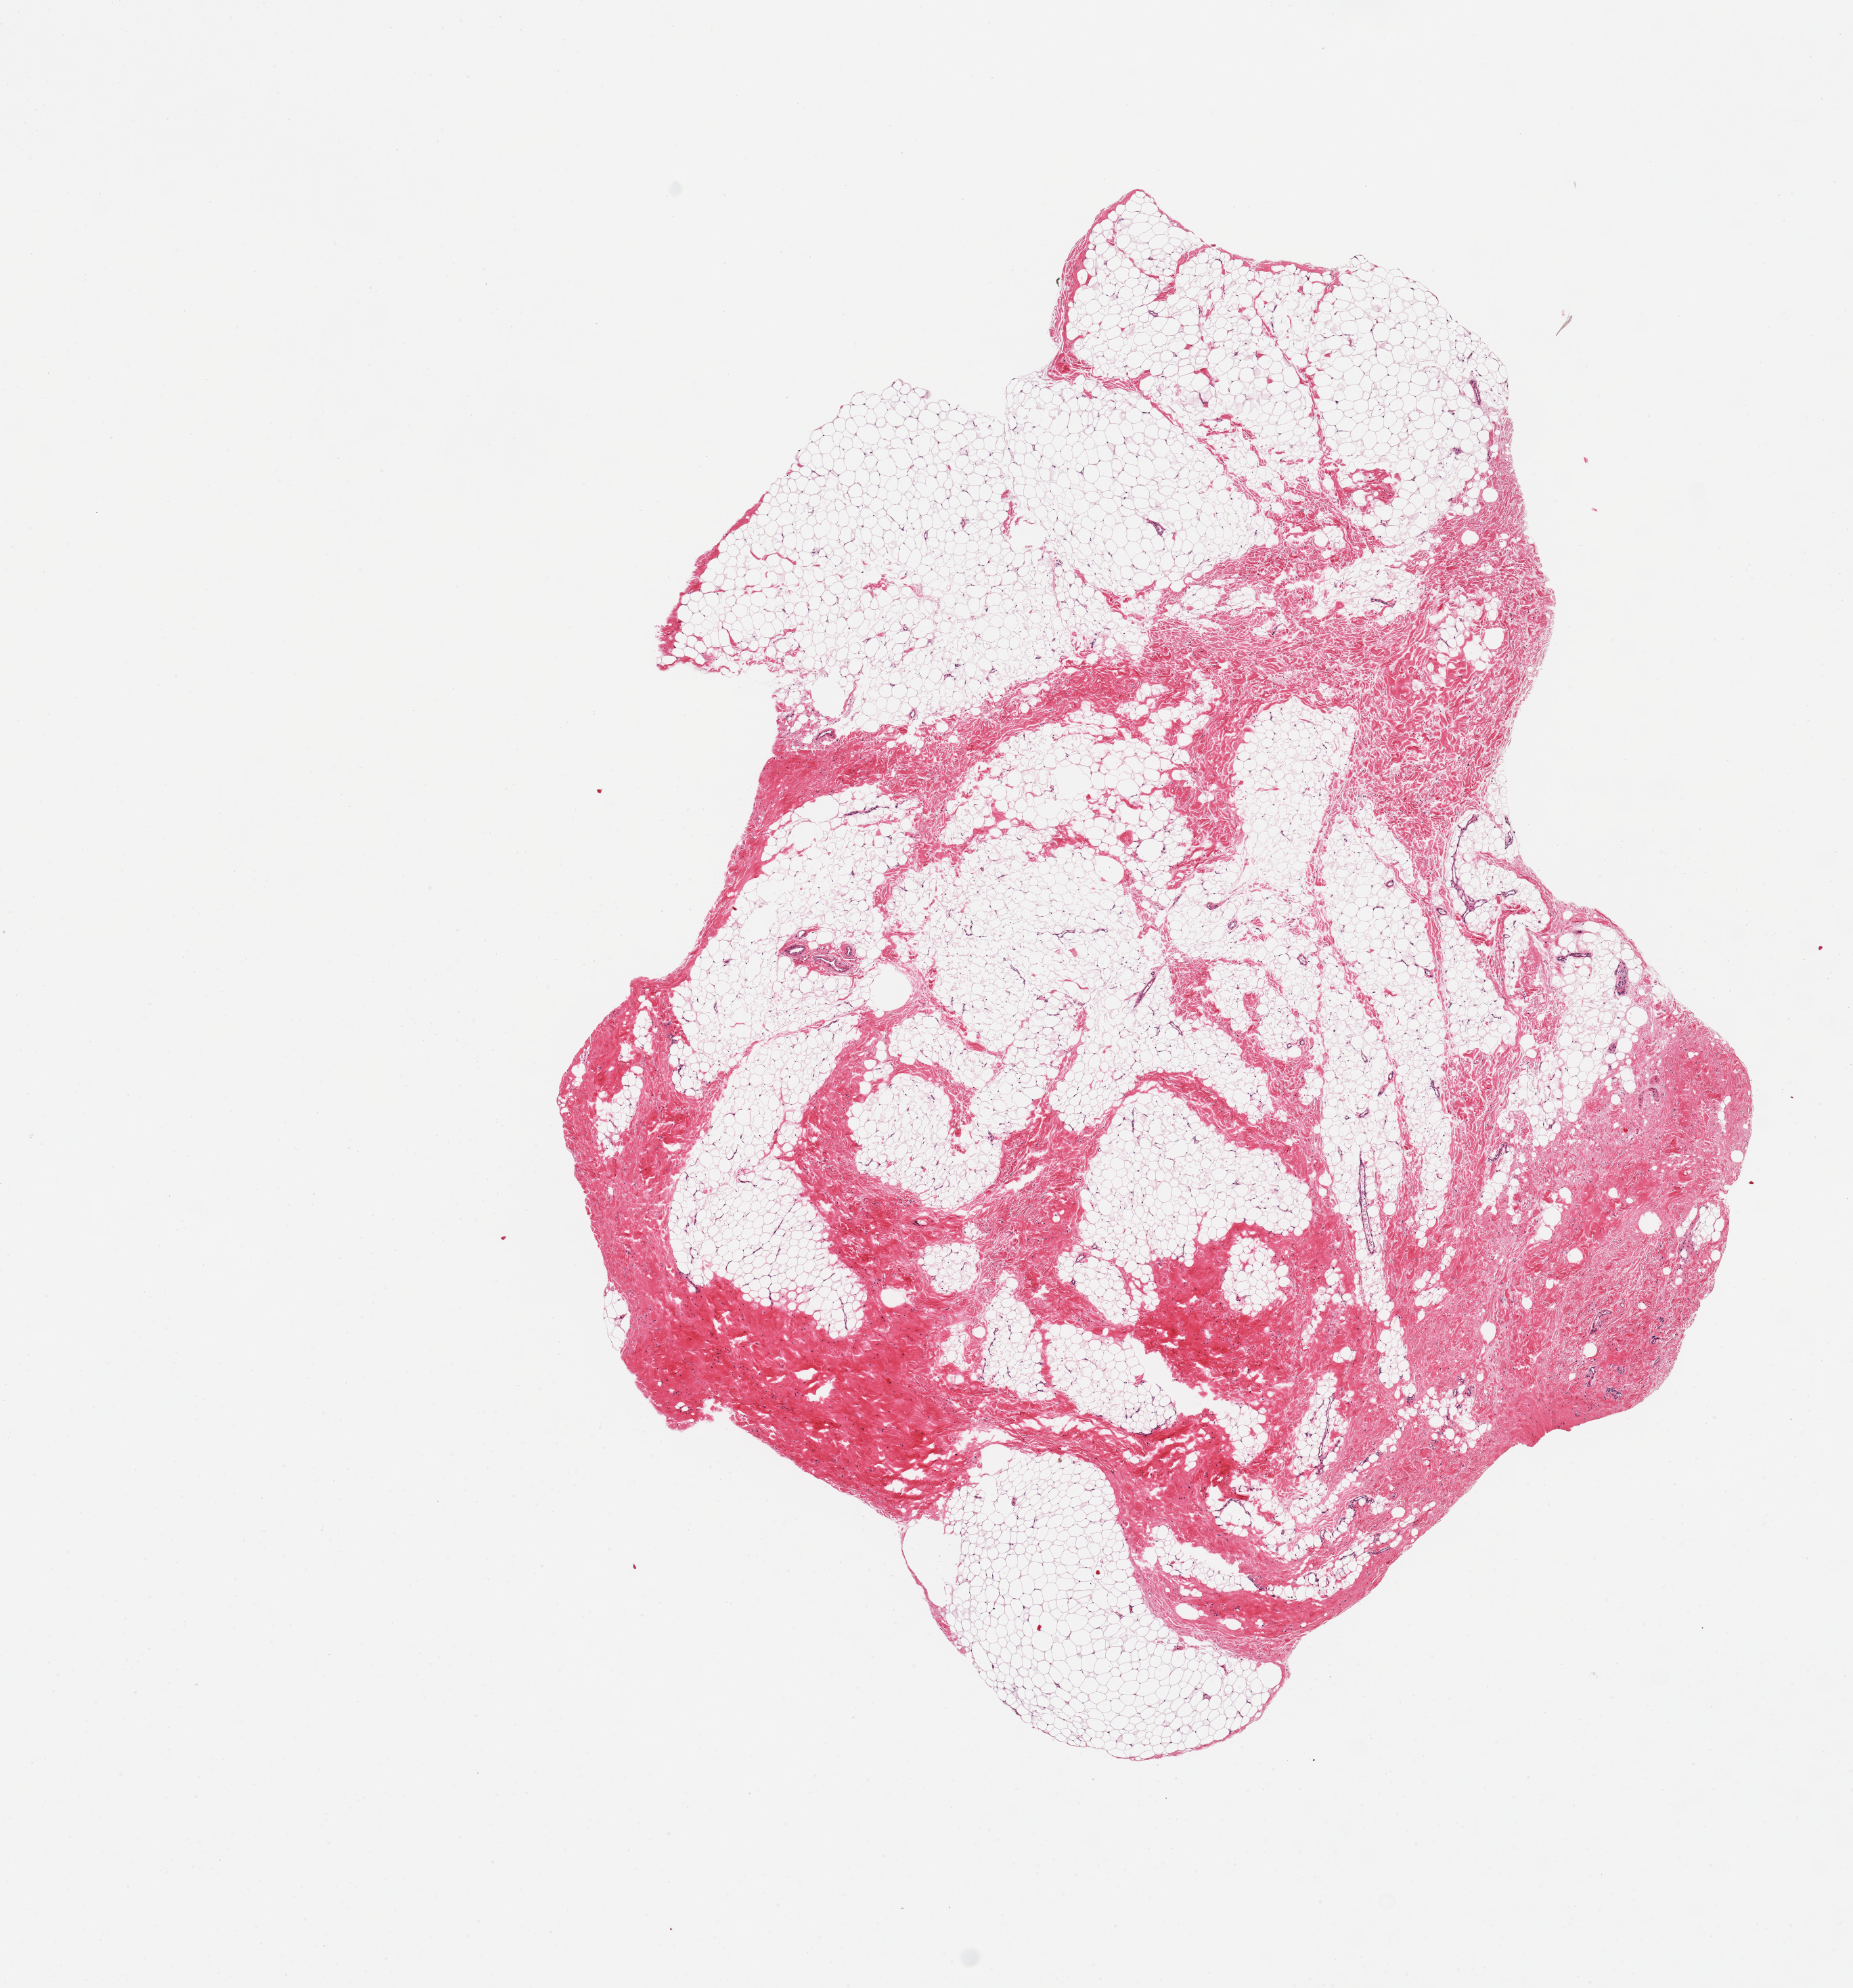
Whole-slide image, H&E stain, brightfield — shown as a low-resolution overview of the whole scanned area (about 10.8 x 11.6 mm), PAXgene-fixed paraffin-embedded (PFPE) section, section of breast (target tissue), donor tissue sample. Male donor.
Pathologist's review note for this sample: 1 pieces; 70% fat, 30% stroma, no ductal elements noted.